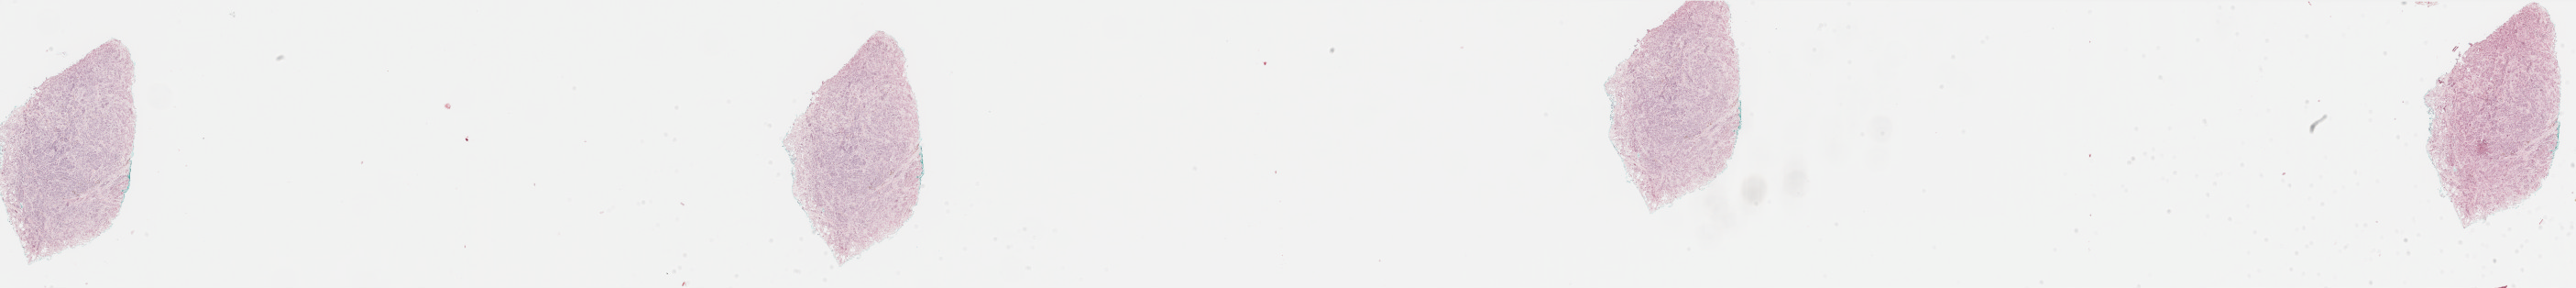
Whole-slide histology image, H&E-stained, shown as a low-resolution overview of the whole scanned area (about 44.6 x 5.0 mm), FFPE section, sample: primary tumour, skin. Patient: male, age at initial diagnosis 81 years.
• histologic diagnosis: Malignant melanoma, NOS